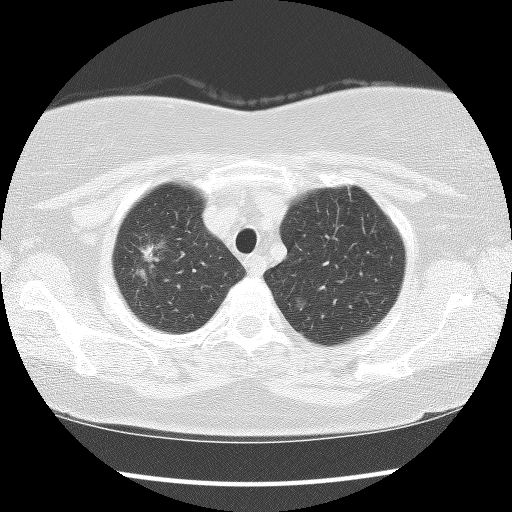
Chest CT (low-dose screening protocol), one axial image. Second screening round (one year after baseline). Lung window (W 1500 / L -600 HU). Lung (sharp) reconstruction kernel (BONE). 120 kVp. Slice 6 of 79 in the series. 512 × 512 image matrix, field of view 326 × 326 mm. Female participant, aged 67 years at enrolment. Former smoker at enrolment.
Expert reader's lesion annotation, box from (x=112, y=229) to (x=169, y=291) px. The screening reader recorded 3 non-calcified nodules or masses ≥4 mm on this exam (right upper lobe, right lower lobe, right upper lobe); which of them this box marks is not recorded. Official screen result: positive, other. Participant outcome: lung cancer diagnosed 56 days after this screen — adenocarcinoma with mixed subtypes, right upper lobe, poorly differentiated (G3), stage IA (AJCC 6th edition), 30 mm at pathology.